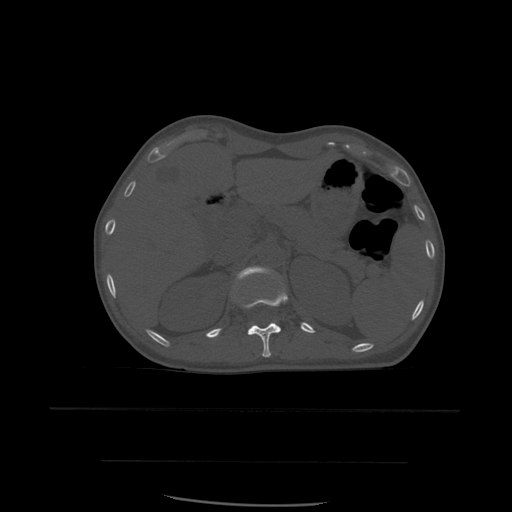
CT including the spine, one axial slice. Slice 267 of 574 in the series (ordered by position). Bone window (W 1800 / L 400 HU). 1.25 mm slice thickness. 512 × 512 image matrix. Patient age 48 years. Case-level facts recorded for this patient, not image findings: primary cancer: lung.
Outlined on this slice (semi-automatic segmentation, software-assisted and operator-edited):
- L1 vertebra: bounding box (x1, y1, x2, y2) in pixels: (237, 266, 272, 280)
- T12 vertebra: (241, 288, 289, 358)